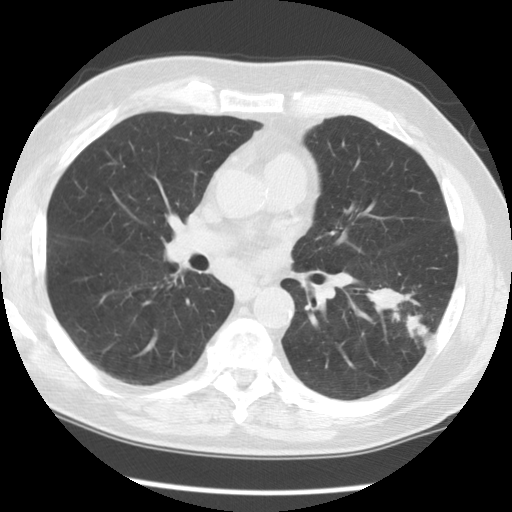
Low-dose screening chest CT, one axial slice. Position 73 of 130 along the scan axis. Lung window (W 1500 / L -600 HU). 512 × 512 image matrix.
Annotated regions visible in this slice (expert manual segmentation):
- lesion 1 (tumor, lower lobe of left lung): bounding box (x1, y1, x2, y2) in pixels: (367, 288, 432, 347)